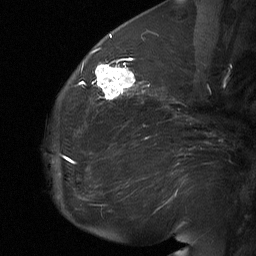
Breast MRI (dynamic contrast-enhanced), one sagittal slice; slice 24 of 64 in the series (ordered by position); dynamic contrast-enhanced study with each time point stored as its own series, time point 2 of 3 at this slice position (early post-contrast, ordered by acquisition time); 1.5 T; TE 4.8 ms, TR 27 ms; 2 mm slice thickness; 256 × 256 image matrix, field of view 200 × 200 mm. Patient: female, 60 years. Case-level facts recorded for this patient, not image findings: setting: breast cancer imaged before/during neoadjuvant chemotherapy; receptor status: HR-positive, HER2-negative.
Annotated regions visible in this slice (semi-automatically segmented with operator editing):
- analysis volume of interest (the breast-tissue region the enhancement analysis was run in; not a lesion): box from (x=91, y=56) to (x=139, y=104) px
- tumour enhancement mask (voxels above the 90 % enhancement threshold inside the analysis volume of interest): (x=95, y=61)–(x=135, y=100)